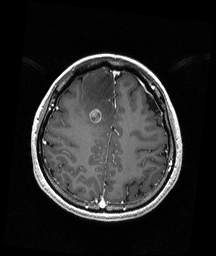
Brain MRI from a brain-tumour surgery series, one axial slice. Position 57 of 192 along the scan axis. T1-weighted post-contrast. 1 mm slice thickness. 216 × 256 image matrix. Case-level facts recorded for this patient, not image findings: histopathology: Astrocytoma; WHO grade: 4; IDH mutation: yes.
Annotated regions visible in this slice (outlined manually by an expert reader):
- tumour: box from (x=90, y=108) to (x=102, y=123) px